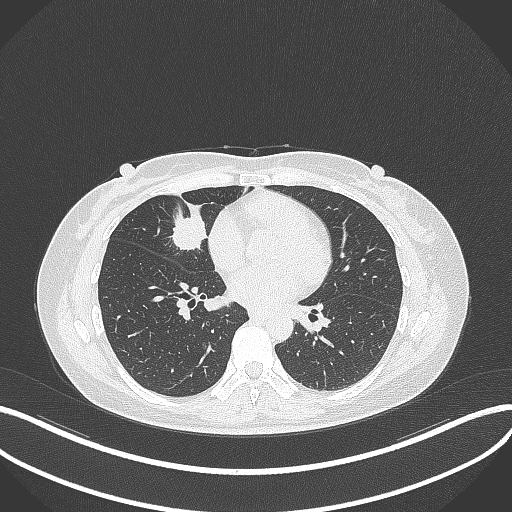
Chest CT, one axial slice; reconstruction kernel B70f; 120 kVp; lung window (W 1500 / L -600 HU); 1 mm slice thickness; 512 × 512 image matrix, field of view 400 × 400 mm. Patient: female, 43 years. Case-level facts recorded for this patient, not image findings: clinical TNM (as recorded): T1c N3 M1; histopathological grade: G1.
Outlined on this slice (bounding box drawn by a radiologist):
- lung tumour (recorded histology: adenocarcinoma): bounding box (x1, y1, x2, y2) in pixels: (166, 201, 208, 254)